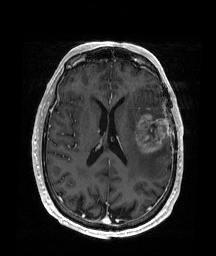
Brain MRI from a brain-tumour surgery series, one axial slice; T1-weighted post-contrast; 216 × 256 image matrix, field of view 219 × 260 mm. From the clinical record (not read from this slice): histopathology: Glioblastoma; WHO grade: 4; IDH mutation: no.
Annotated regions visible in this slice (manually delineated by an expert):
- tumour: bounding box <135,113,169,154> (left, top, right, bottom; pixels)